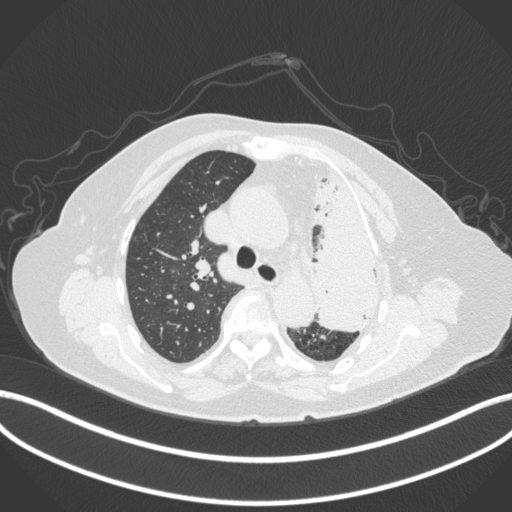
Chest CT, one axial slice; position 279 of 399 along the scan axis; reconstruction kernel B31f; 120 kVp; lung window (W 1500 / L -600 HU); 1 mm slice thickness; 512 × 512 image matrix, field of view 400 × 400 mm. Female patient, age 75 years. Case-level facts recorded for this patient, not image findings: clinical TNM (as recorded): T3 N3 M1.
Outlined on this slice (rectangle marked by the reading radiologist):
- lung tumour (recorded histology: adenocarcinoma): bounding box [x1, y1, x2, y2] px = [301, 159, 385, 336]